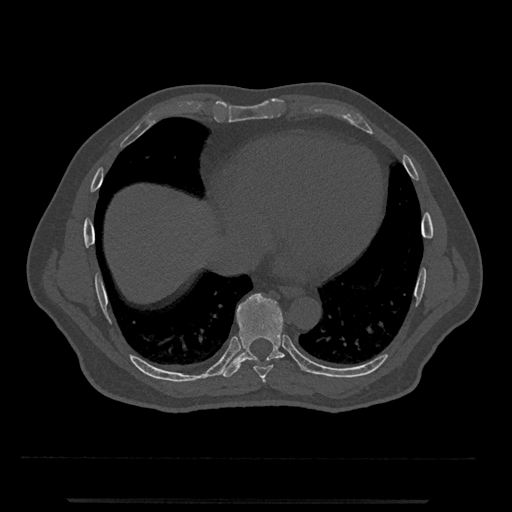
CT including the spine, one axial slice; reconstruction kernel Br40s/3; 120 kVp; bone window (W 1800 / L 400 HU); 0.5 mm slice thickness; 512 × 512 image matrix. Male patient, age 63 years. Case-level facts recorded for this patient, not image findings: primary cancer: prostate.
Structures marked on this image (semi-automatic segmentation, software-assisted and operator-edited):
- T7 vertebra: bounding box <262,376,266,383> (left, top, right, bottom; pixels)
- T8 vertebra: <254,361,273,379>
- T9 vertebra: <221,293,303,378>